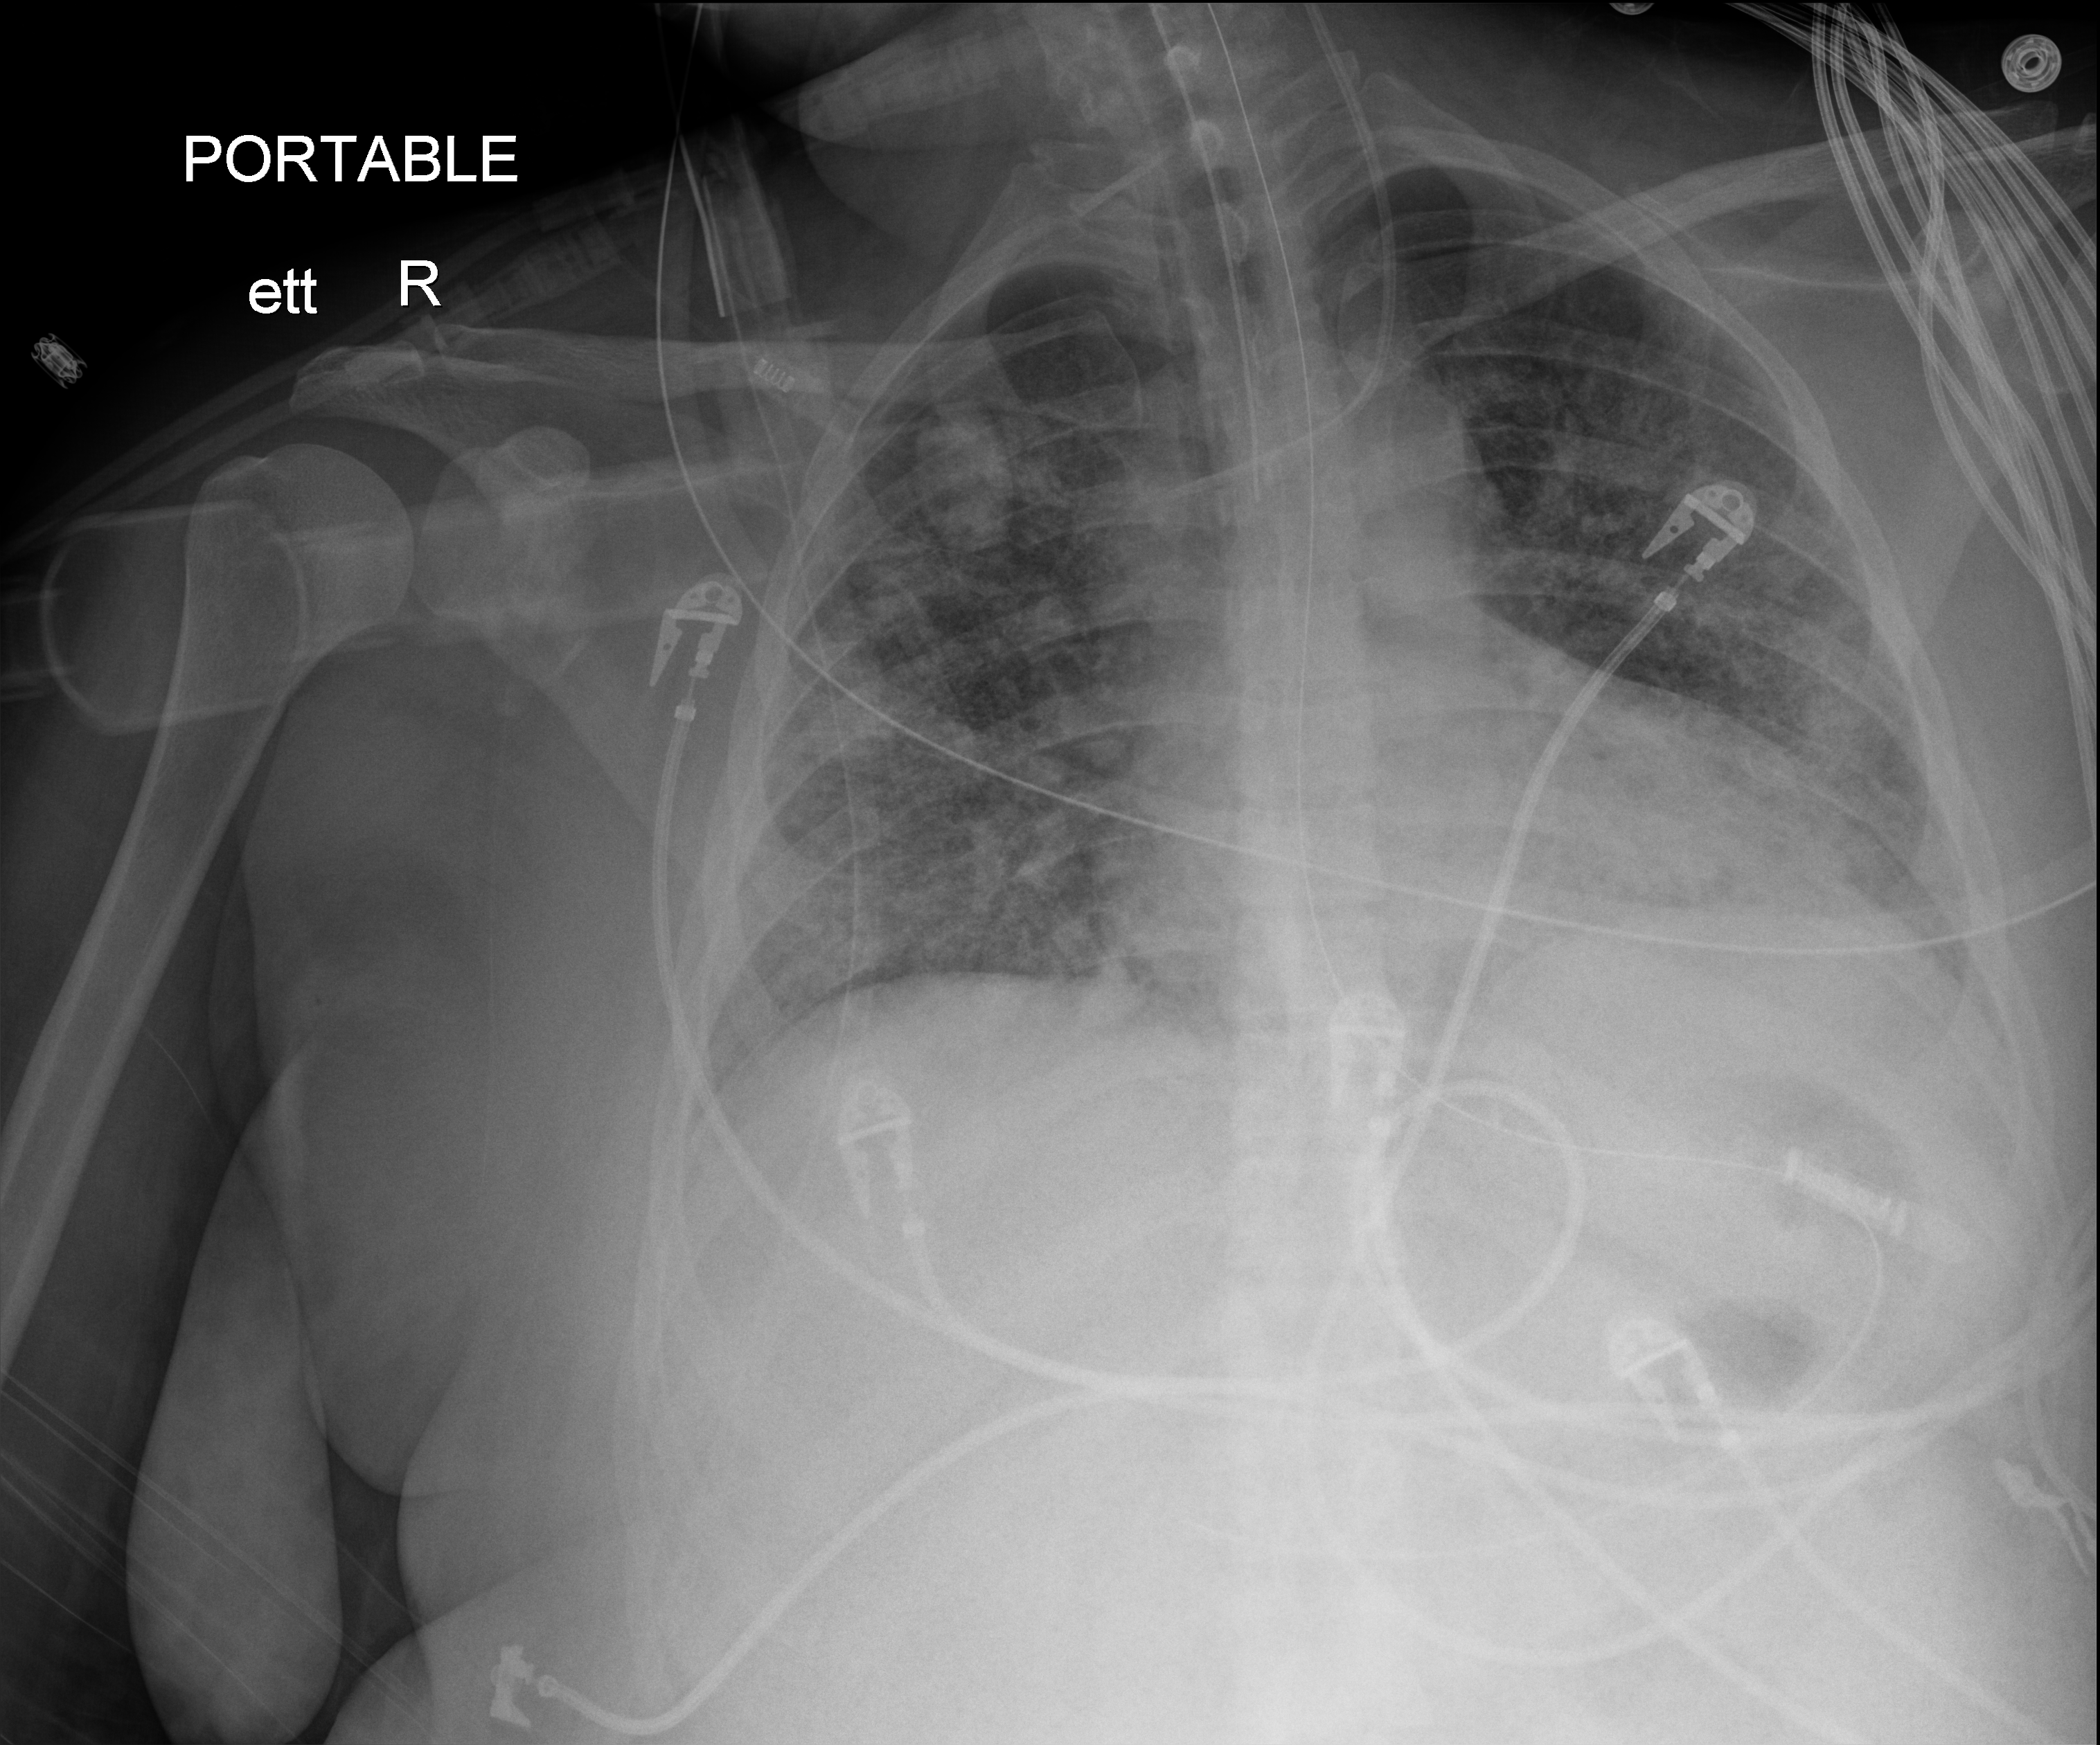
Portable chest radiograph, anteroposterior (AP) projection. Female patient hospitalised with COVID-19, age 18–59 years.
Hospital-stay facts (about this admission, not read from this image; timing relative to this image not recorded): admitted to intensive care during this hospital stay: no.